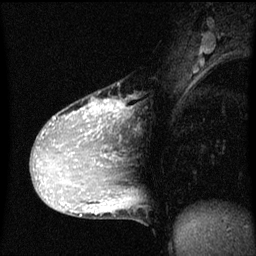
Breast MRI (dynamic contrast-enhanced), one sagittal slice. Position 31 of 60 along the scan axis. Dynamic contrast-enhanced series, image 2 of 3 at this slice position (ordered by acquisition). 1.5 T. TE 4.2 ms, TR 8 ms. 2 mm slice thickness. 256 × 256 image matrix, field of view 200 × 200 mm. Female patient, age 36 years.
Annotated regions visible in this slice (semi-automatic segmentation, software-assisted and operator-edited):
- analysis volume of interest (the breast-tissue region the enhancement analysis was run in; not a lesion): box from (x=33, y=98) to (x=121, y=169) px
- tumour enhancement mask (voxels above the 70 % enhancement threshold inside the analysis volume of interest): (x=40, y=100)–(x=121, y=165)